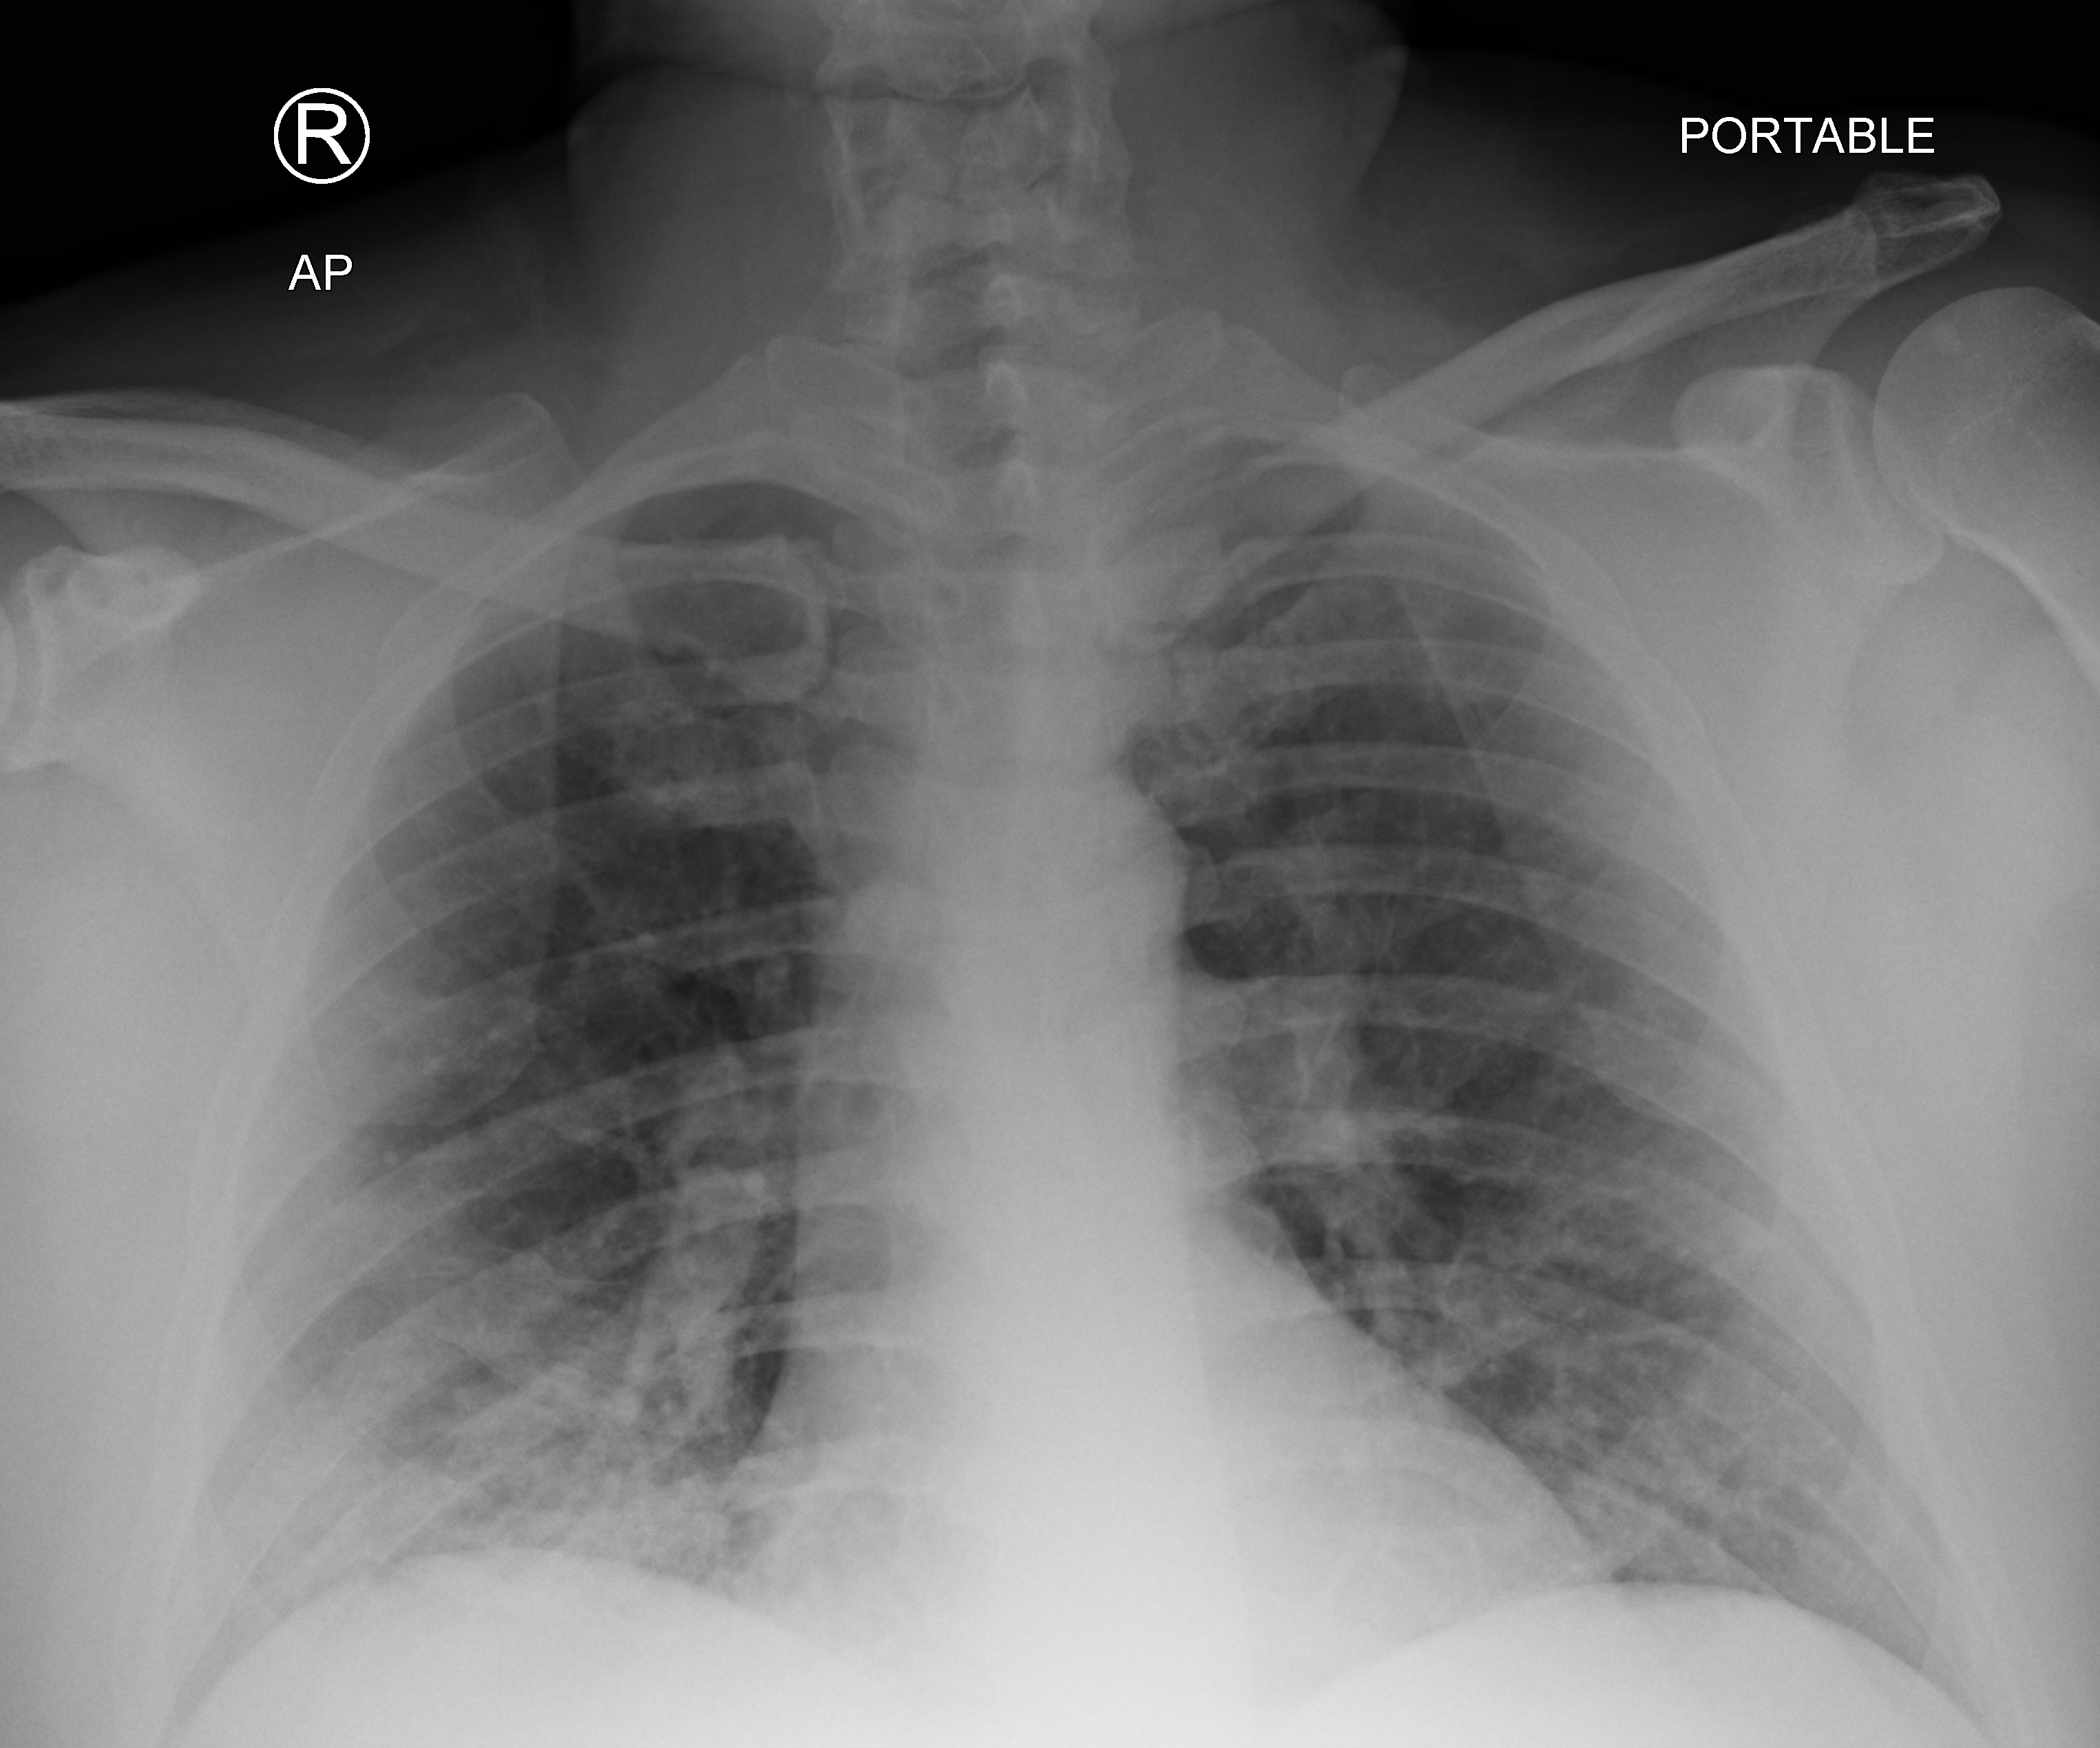
Bedside chest radiograph (computed radiography). Patient hospitalised with COVID-19; male, aged 18–59 years.
Hospital-stay facts (about this admission, not read from this image; timing relative to this image not recorded): diabetes (admission record): no; admitted to intensive care during this hospital stay: no; mechanically ventilated during this hospital stay: no.